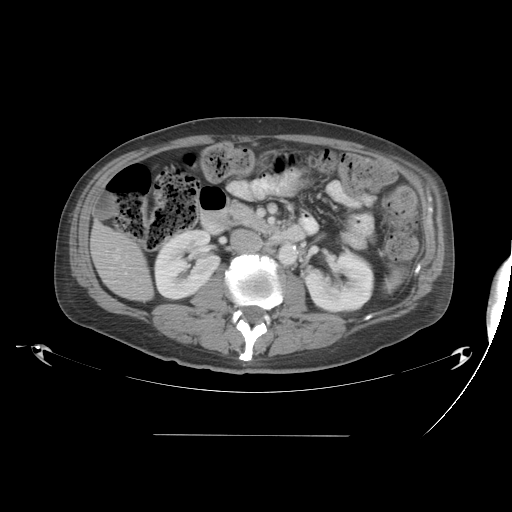
Contrast-enhanced abdominal CT, one axial slice. Slice 15 of 48 in the series (ordered by position). Reconstruction kernel STANDARD. 120 kVp. Intravenous contrast given. Soft-tissue window (W 400 / L 40 HU). 5 mm slice thickness. 512 × 512 image matrix, field of view 486 × 486 mm. Male patient, age 65 years. From the clinical record (not read from this slice): diagnosis: colorectal cancer liver metastases, imaged before liver resection; multiple liver metastases: yes; largest metastasis: 11 cm.
Structures marked on this image (manually delineated by an expert):
- liver: bounding box [x1, y1, x2, y2] px = [92, 225, 153, 302]